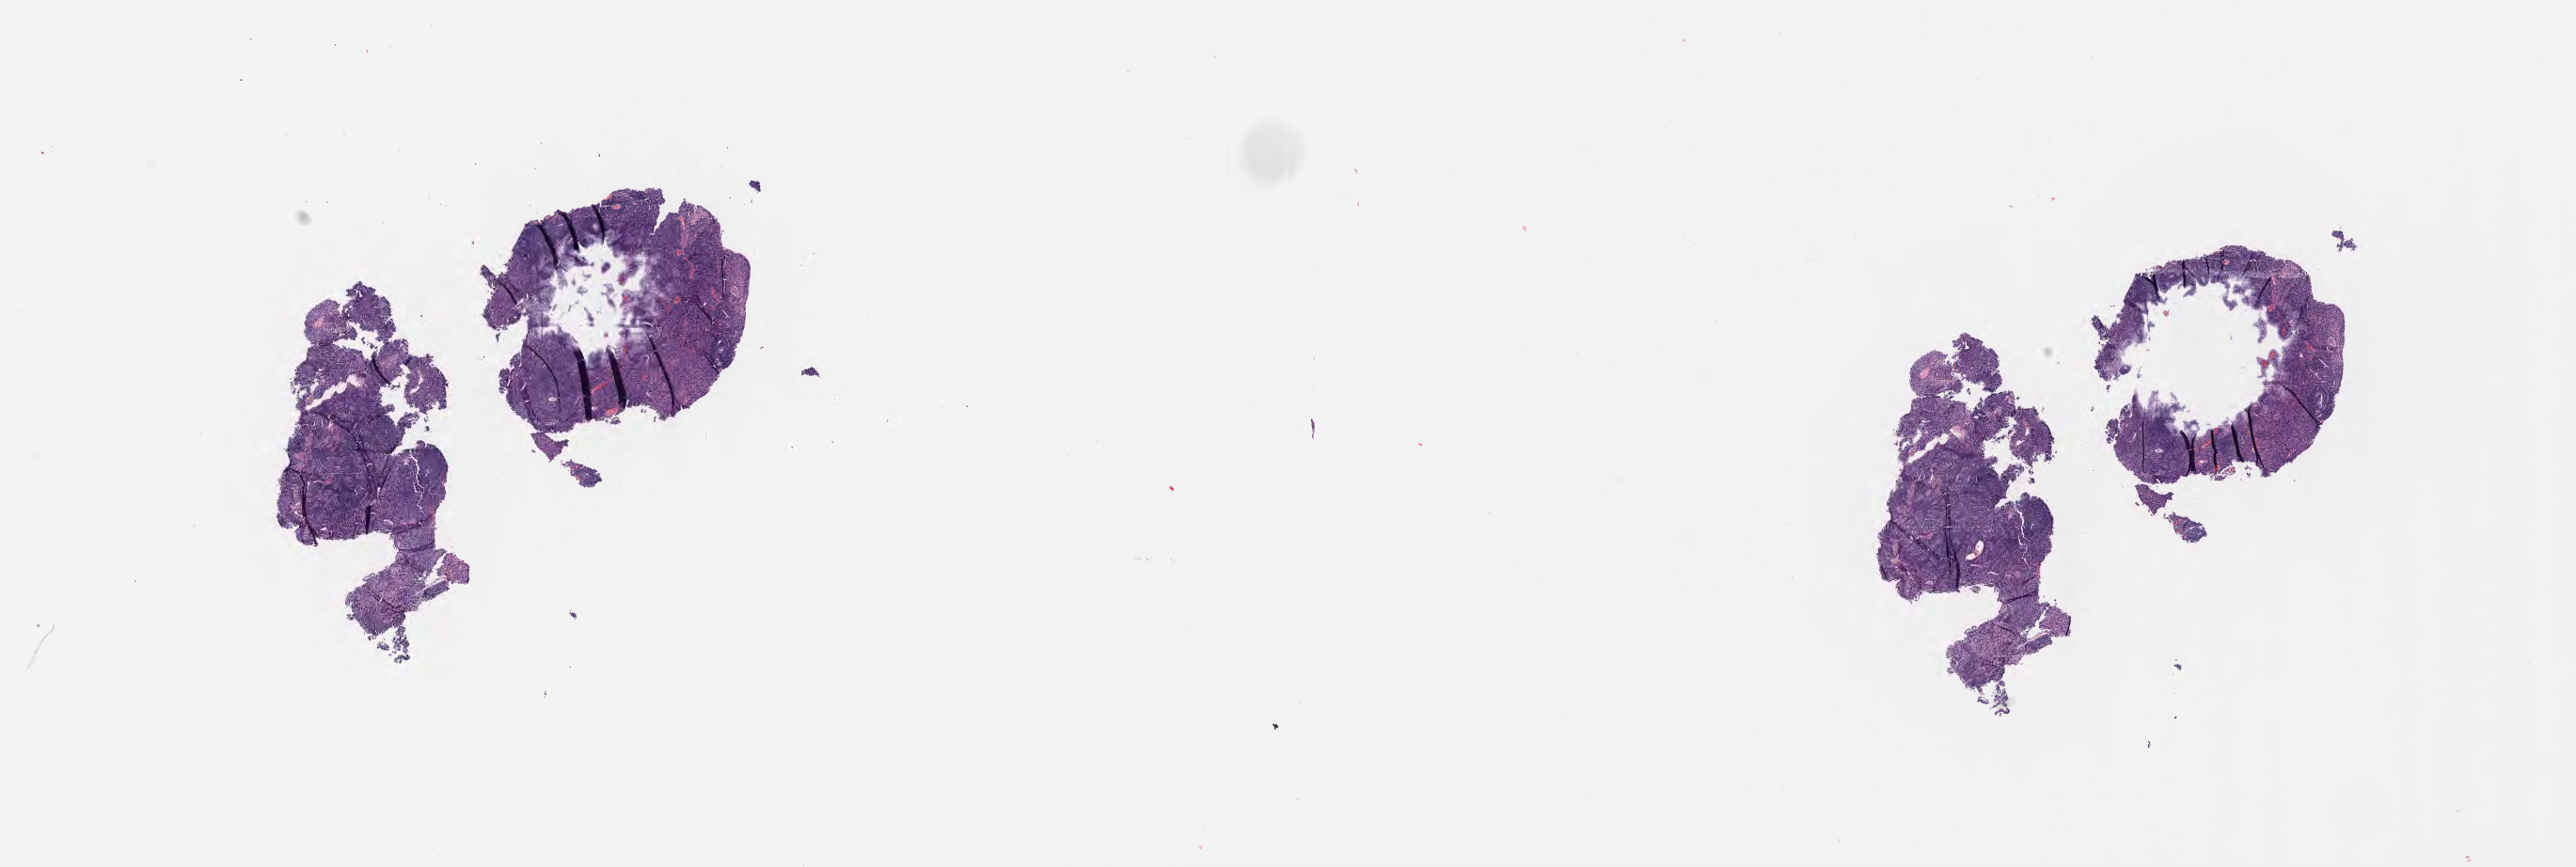
H&E whole-slide image, low-resolution overview of the scanned area, about 22.1 x 7.4 mm, tumor tissue, anatomic site: cervix. Female patient, aged 44.
Diagnosis: Squamous cell carcinoma, large cell, nonkeratinizing, NOS.